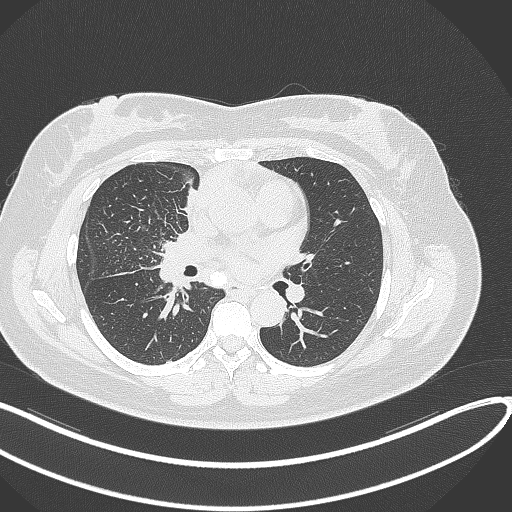
Chest CT, one axial slice. Position 141 of 303 along the scan axis. Reconstruction kernel B70f. 120 kVp. Lung window (W 1500 / L -600 HU). 1 mm slice thickness. 512 × 512 image matrix. Patient: female, 46 years. Case-level facts recorded for this patient, not image findings: clinical TNM (as recorded): T2a N1 M0.
Structures marked on this image (rectangle marked by the reading radiologist):
- lung tumour (recorded histology: adenocarcinoma): bounding box [x1, y1, x2, y2] px = [177, 186, 200, 218]